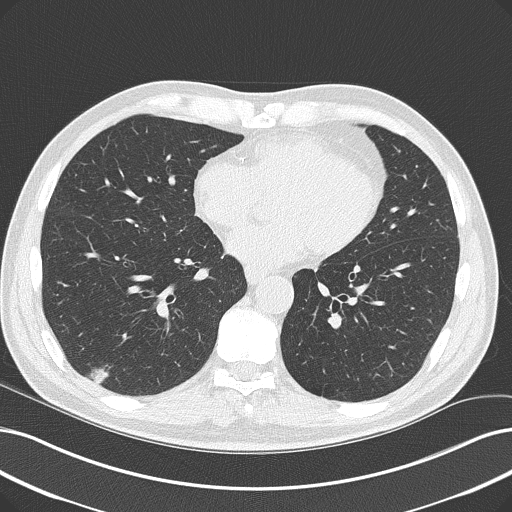
Low-dose screening chest CT, one axial slice; slice 94 of 228 in the series (ordered by position); reconstruction kernel B50f; 120 kVp; lung window (W 1500 / L -600 HU); 2 mm slice thickness; 512 × 512 image matrix, field of view 366 × 366 mm.
Outlined on this slice (manually delineated by an expert):
- lesion 1 (tumor, lower lobe of right lung): bounding box [x1, y1, x2, y2] px = [89, 369, 117, 385]